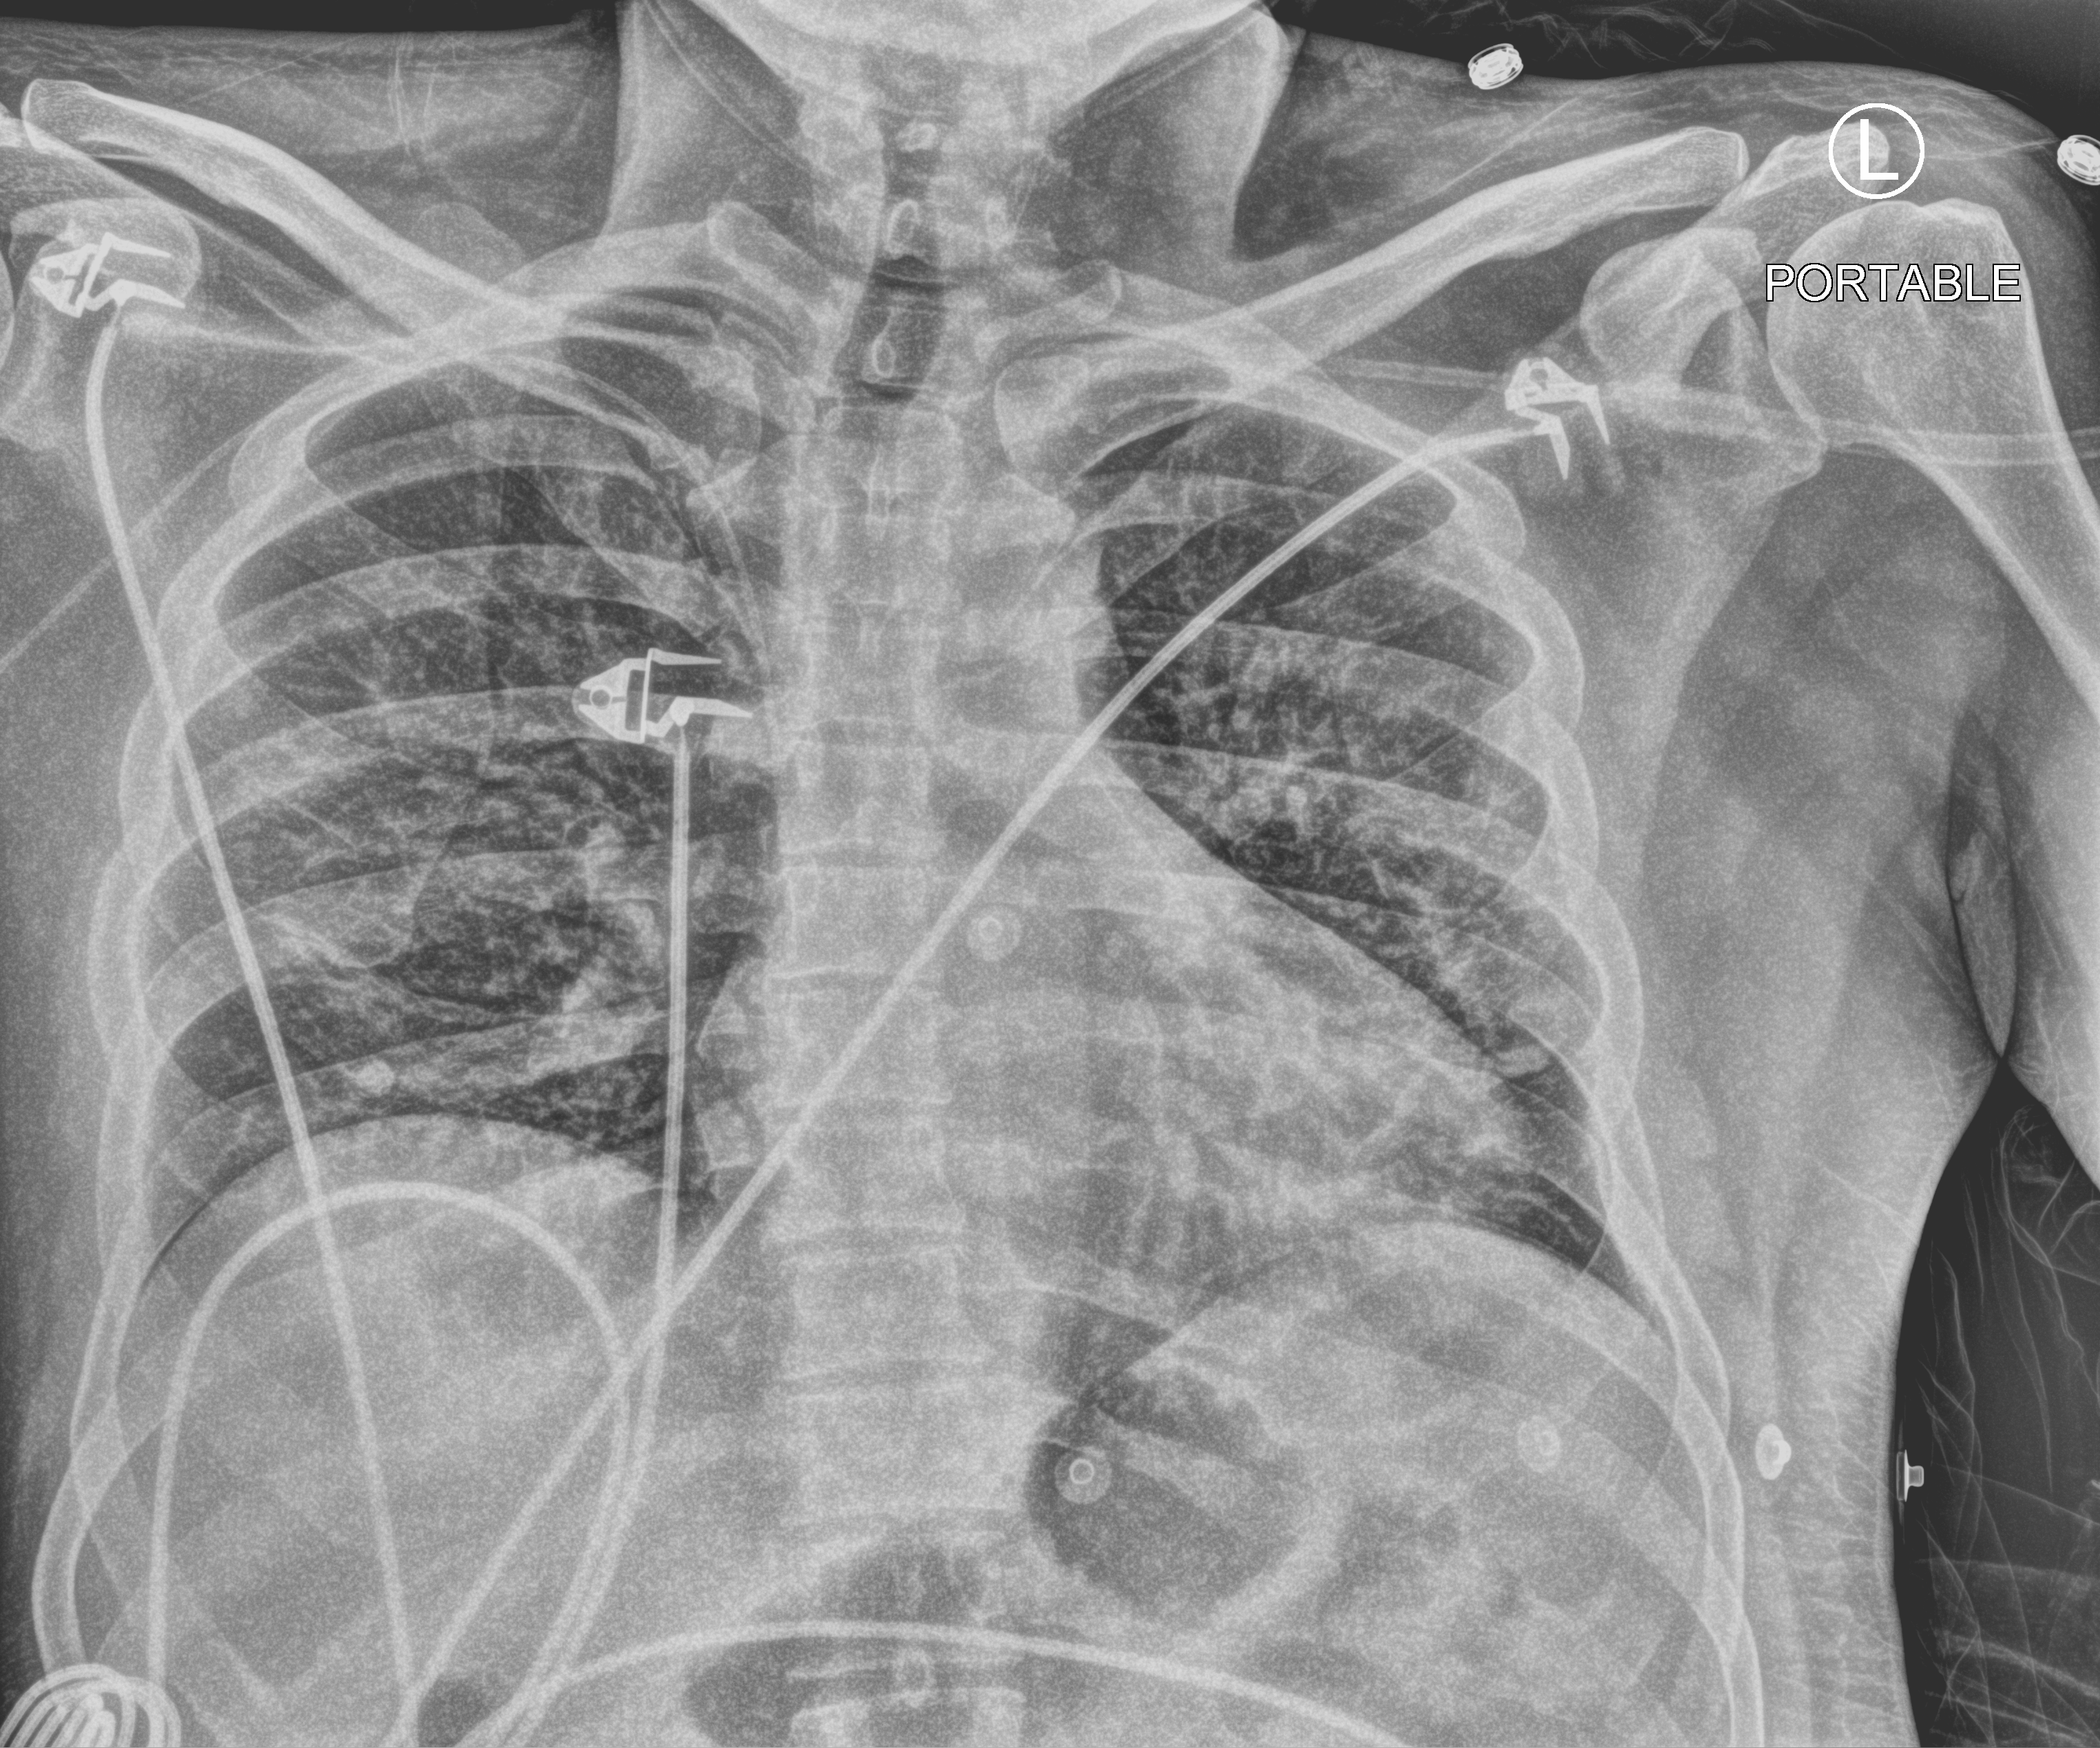
Bedside chest radiograph (computed radiography), anteroposterior (AP) projection. Male patient hospitalised with COVID-19, age 18–59 years.
From the hospital-stay record, not from the radiograph (when in the stay this image was taken is not recorded): admitted to intensive care during this hospital stay: no; mechanically ventilated during this hospital stay: yes.